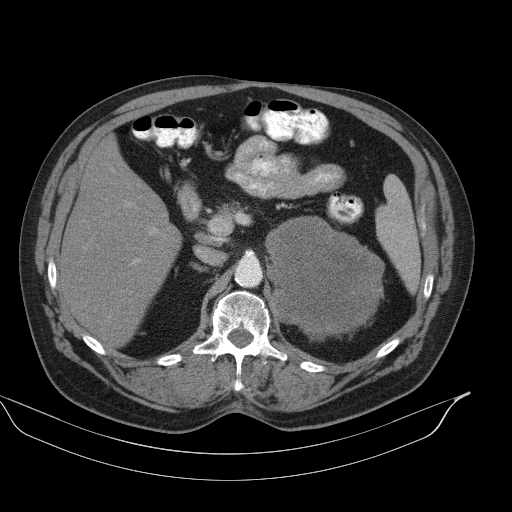
Contrast-enhanced abdominal CT, one axial slice; slice 65 of 92 in the series (ordered by position); reconstruction kernel B41s; intravenous contrast given; soft-tissue window (W 400 / L 40 HU); 5 mm slice thickness; 512 × 512 image matrix, field of view 449 × 449 mm. Male patient, age 56 years. Case-level facts recorded for this patient, not image findings: diagnosis: adrenocortical carcinoma; tumour side: left adrenal; tumour size at pathology: 15 cm; Ki-67 index: 35 %.
Structures marked on this image (semi-automatic segmentation, software-assisted and operator-edited):
- mass: box from (x=266, y=217) to (x=383, y=335) px